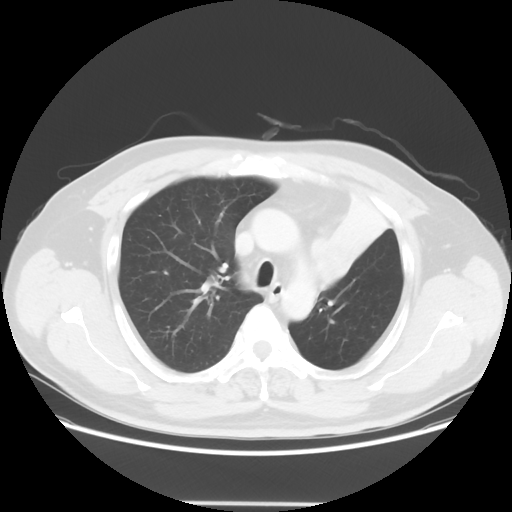
Chest CT, one axial slice; position 43 of 62 along the scan axis; reconstruction kernel STANDARD; 120 kVp; lung window (W 1500 / L -600 HU); 5 mm slice thickness; 512 × 512 image matrix, field of view 403 × 403 mm. Patient: male, 49 years. From the clinical record (not read from this slice): clinical TNM (as recorded): T3 N3 M1c.
Structures marked on this image (rectangle marked by the reading radiologist):
- lung tumour (recorded histology: squamous cell carcinoma): bounding box <304,224,362,295> (left, top, right, bottom; pixels)